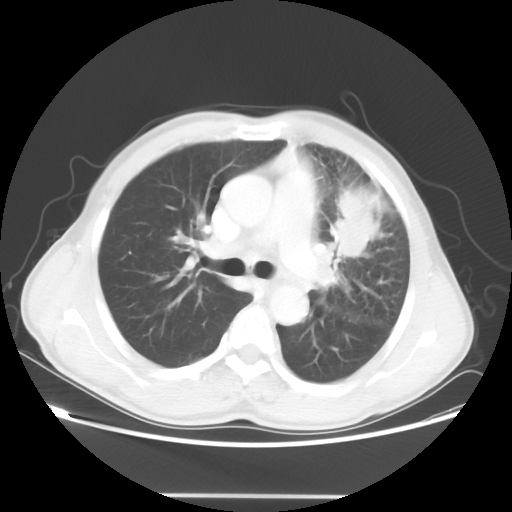
Chest CT, one axial slice. Position 33 of 55 along the scan axis. 100 kVp. Lung window (W 1500 / L -600 HU). 5 mm slice thickness. 512 × 512 image matrix, field of view 398 × 398 mm. Patient: male, 60 years. From the clinical record (not read from this slice): clinical TNM (as recorded): T3 N3 M0.
Structures marked on this image (bounding box drawn by a radiologist):
- lung tumour (recorded histology: adenocarcinoma): box from (x=327, y=174) to (x=385, y=262) px